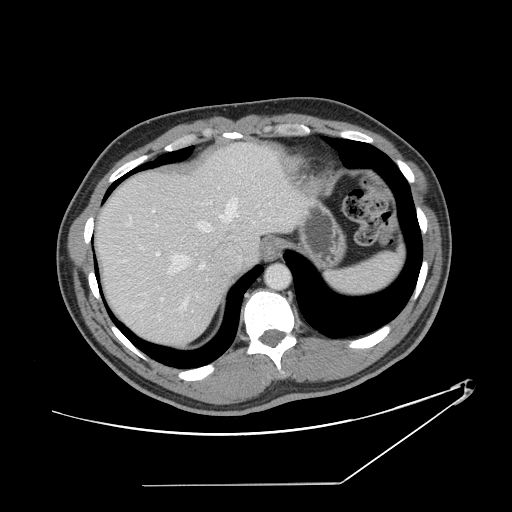
Contrast-enhanced abdominal CT, one axial slice. Slice 119 of 152 in the series (ordered by position). Intravenous contrast given. Soft-tissue window (W 400 / L 40 HU). 2.5 mm slice thickness. 512 × 512 image matrix, field of view 432 × 432 mm. Male patient, age 45 years. From the clinical record (not read from this slice): diagnosis: colorectal cancer liver metastases, imaged before liver resection; multiple liver metastases: no; largest metastasis: 1 cm; chemotherapy before resection: yes.
Structures marked on this image (outlined manually by an expert reader):
- hepatic veins: box from (x=111, y=196) to (x=240, y=311) px
- liver: (x=98, y=146)–(x=304, y=346)
- planned liver remnant (the part of the liver to remain after resection): (x=98, y=168)–(x=233, y=347)
- portal vein (with intrahepatic branches): (x=156, y=252)–(x=208, y=312)